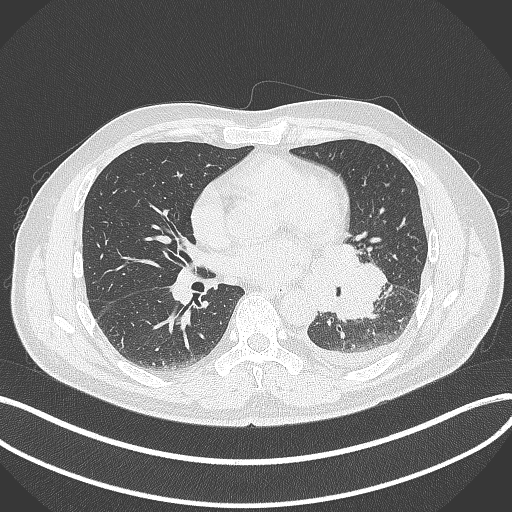
Chest CT, one axial slice; position 172 of 342 along the scan axis; lung window (W 1500 / L -600 HU); 512 × 512 image matrix, field of view 400 × 400 mm. Patient: male, 58 years. From the clinical record (not read from this slice): clinical TNM (as recorded): T3 N1 M1b; histopathological grade: G3.
Structures marked on this image (bounding box drawn by a radiologist):
- lung tumour (recorded histology: small cell carcinoma): bounding box (x1, y1, x2, y2) in pixels: (313, 240, 387, 323)